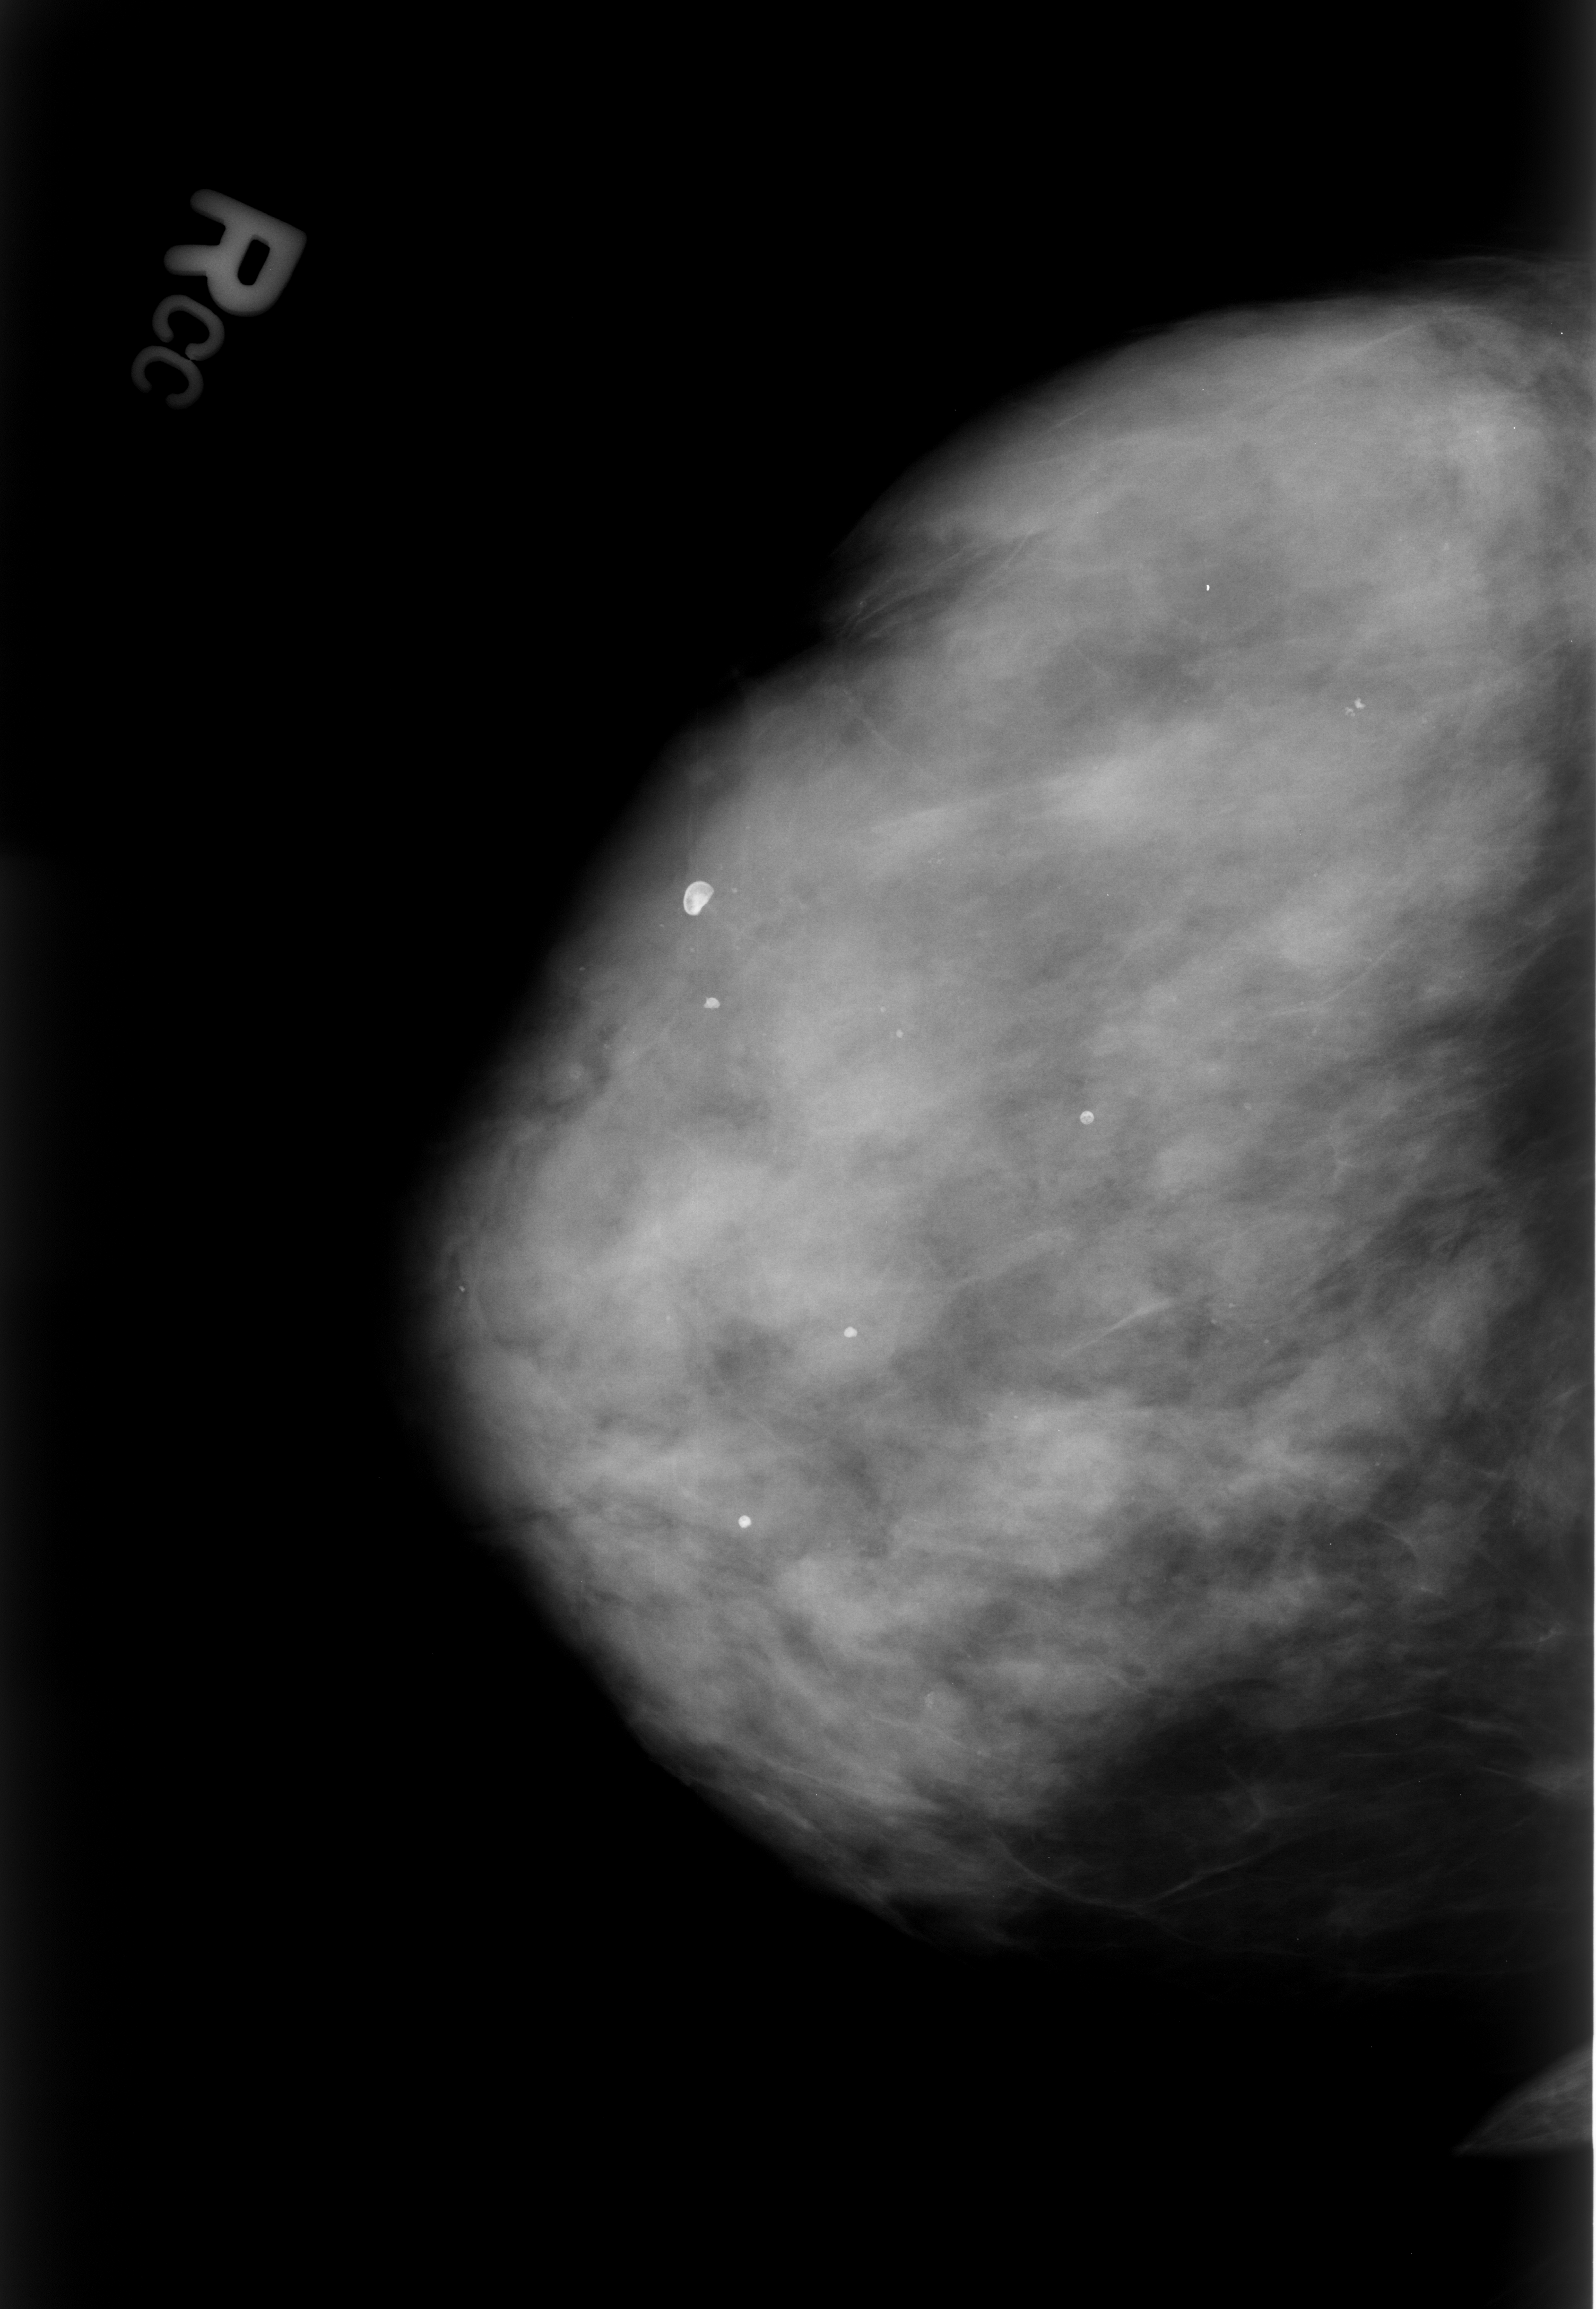
Mammogram (digitized film); right breast; craniocaudal (CC) view; BI-RADS breast density category 4 (scale 1–4); 1596 × 2309 image matrix.
Expert-marked regions of interest on this film, with their recorded descriptors:
- Finding 1 of 6: calcifications, morphology round and regular / lucent center / punctate, distribution diffusely scattered; BI-RADS assessment category 2; subtlety rating 5 on a 1 (subtle) to 5 (obvious) scale; outcome (as recorded, no biopsy): benign without callback (not worked up further): bounding box [x1, y1, x2, y2] px = [662, 865, 731, 935]
- Finding 2 of 6: calcifications, morphology round and regular / lucent center / punctate, distribution diffusely scattered; BI-RADS assessment category 2; benign; no additional work-up was recommended (outcome (as recorded, no biopsy): benign without callback): [687, 988, 748, 1032]
- Finding 3 of 6: calcifications, morphology round and regular / lucent center / punctate, distribution diffusely scattered; BI-RADS assessment category 2; subtlety rating 5 on a 1 (subtle) to 5 (obvious) scale; benign; no additional work-up was recommended (outcome (as recorded, no biopsy): benign without callback): [721, 1502, 782, 1550]
- Finding 4 of 6: calcifications, morphology round and regular / lucent center / punctate, distribution diffusely scattered; BI-RADS assessment category 2; subtlety rating 5 on a 1 (subtle) to 5 (obvious) scale; benign; no additional work-up was recommended (outcome (as recorded, no biopsy): benign without callback): [827, 1307, 888, 1355]
- Finding 5 of 6: calcifications, morphology round and regular / lucent center / punctate, distribution diffusely scattered; BI-RADS assessment category 2; subtlety rating 5 on a 1 (subtle) to 5 (obvious) scale; outcome (as recorded, no biopsy): benign without callback (not worked up further): [1061, 1082, 1117, 1156]
- Finding 6 of 6: calcifications, morphology round and regular / lucent center / punctate, distribution diffusely scattered; BI-RADS assessment category 2; benign; no additional work-up was recommended (outcome (as recorded, no biopsy): benign without callback): [1320, 678, 1393, 735]